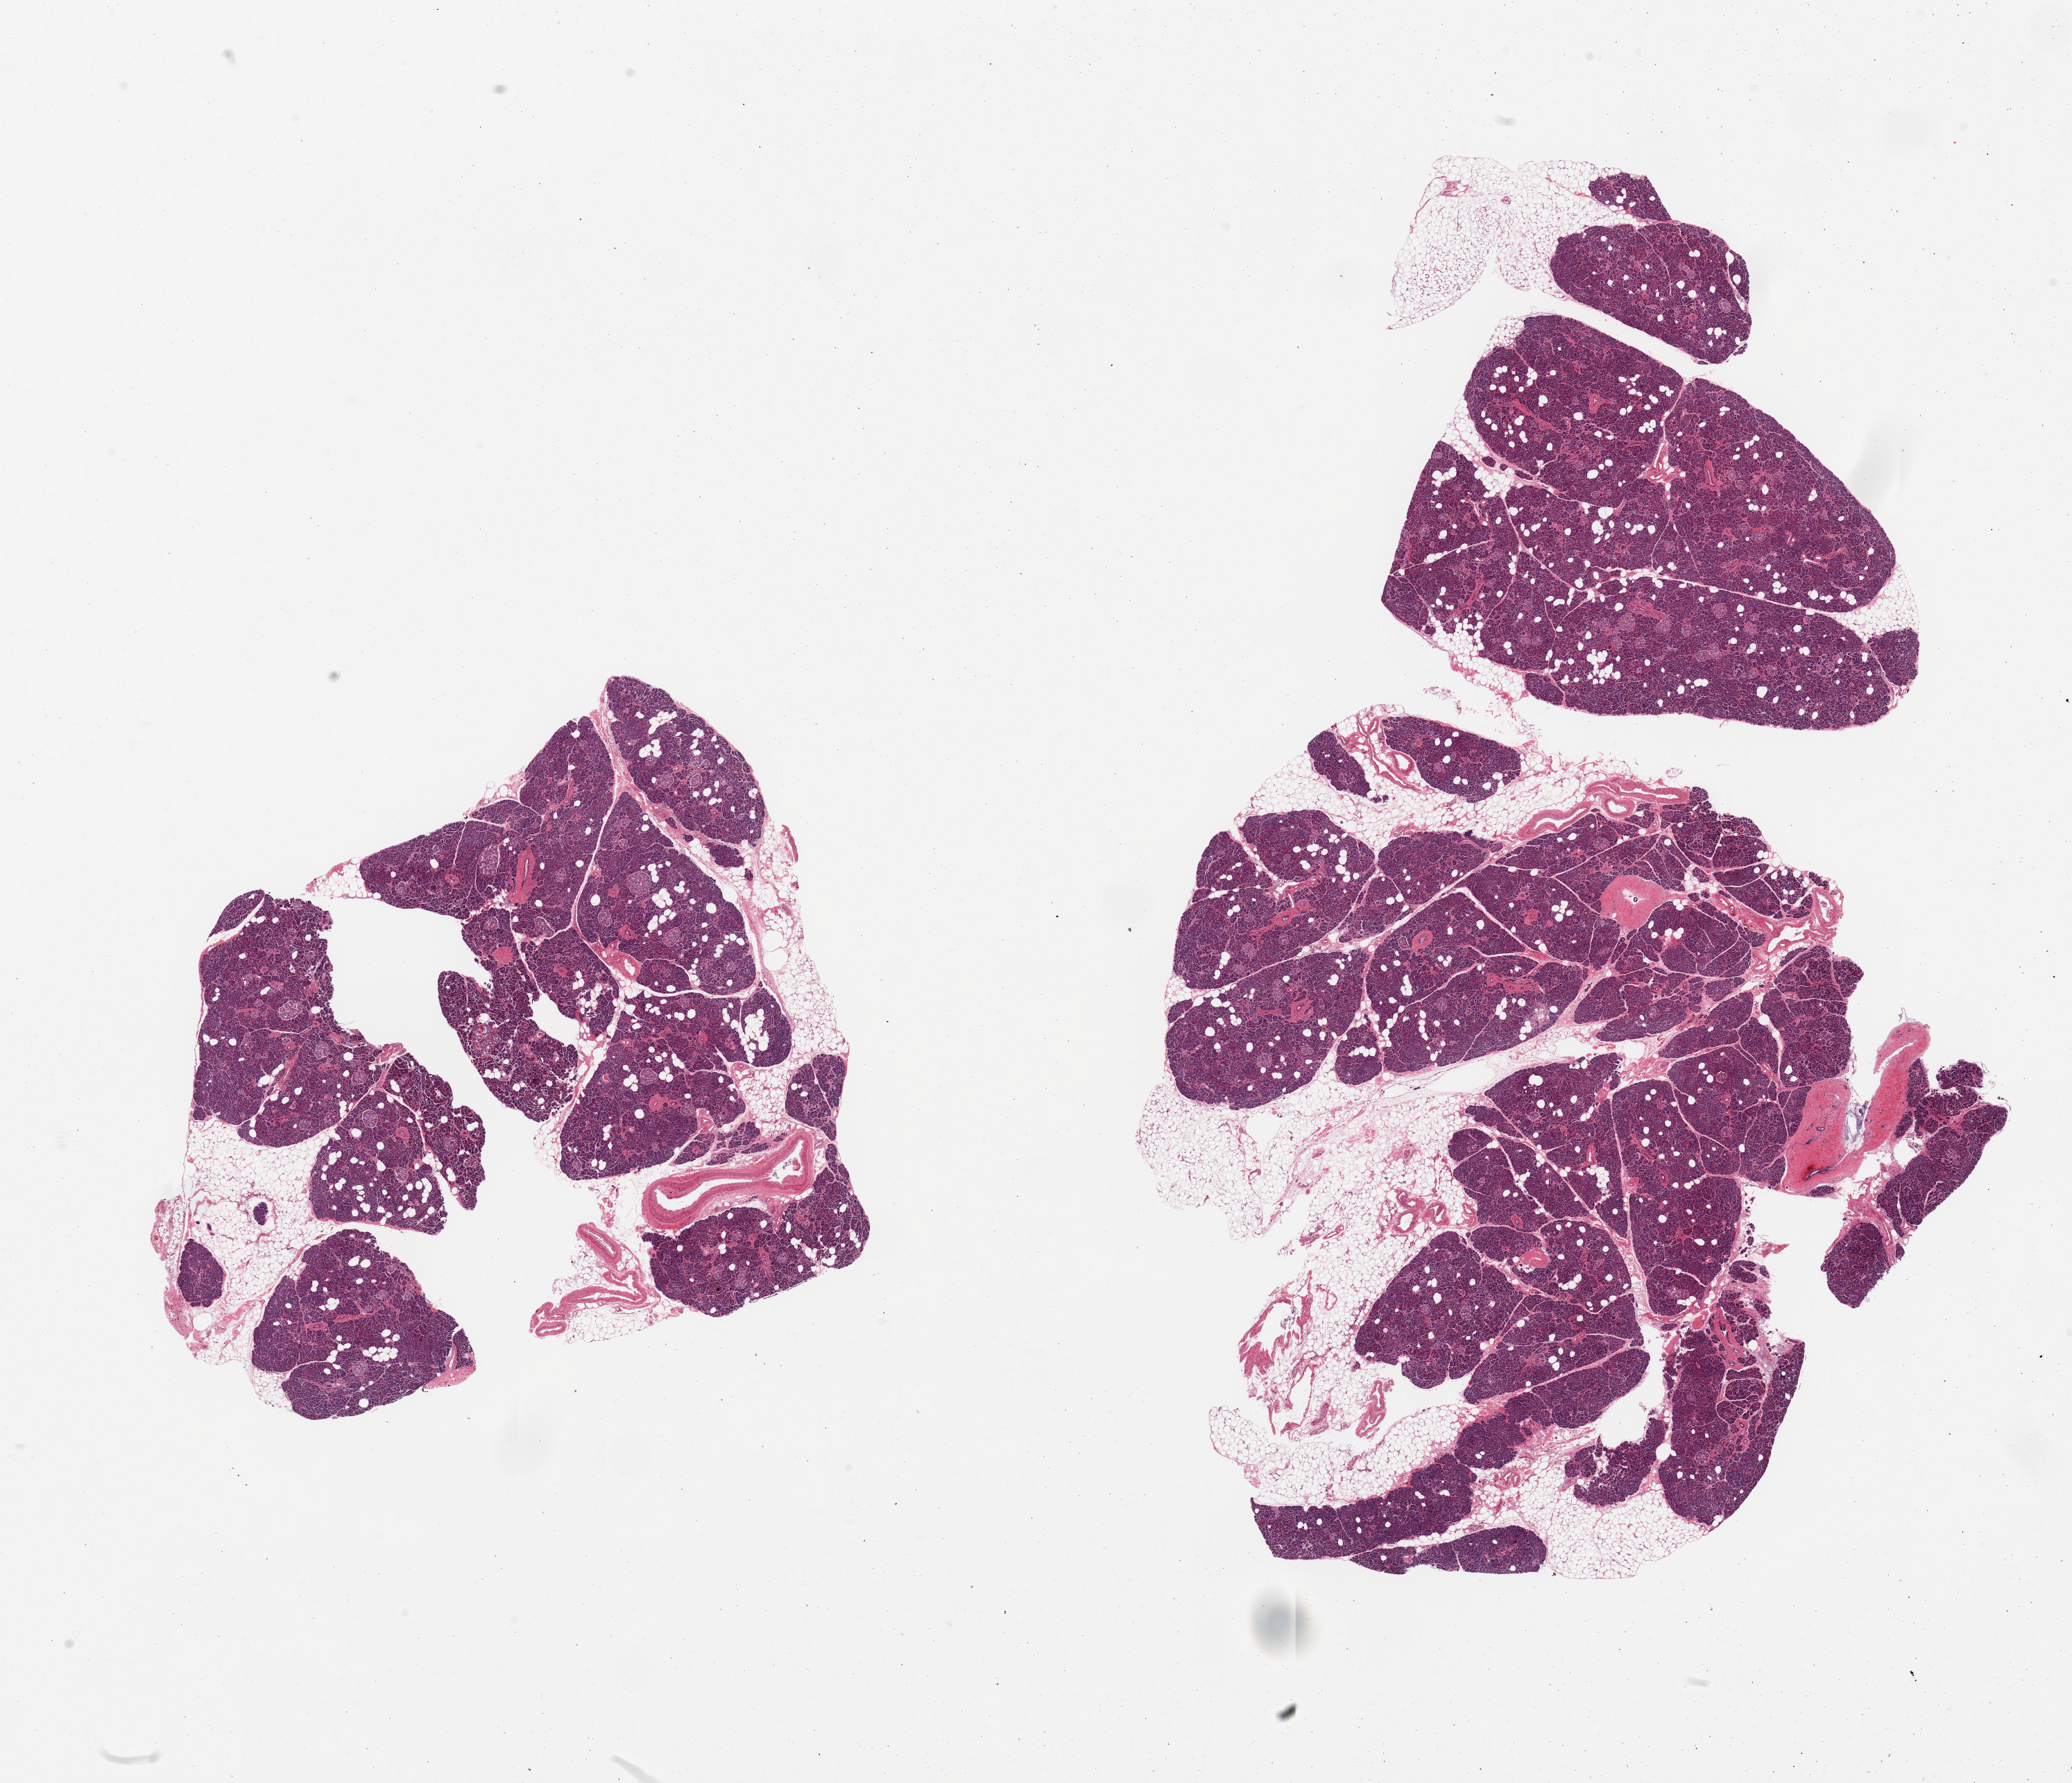
Whole-slide image, H&E stain, brightfield, shown as a low-resolution overview of the whole scanned area (about 23.6 x 20.3 mm, slide scanned at 20x), PAXgene-fixed, paraffin-embedded tissue, sampled site (target tissue): pancreas, tissue donor sample. Donor: male.
Reviewer comment on this tissue sample: 2 pieces; 20% internal fat; numerous islets.